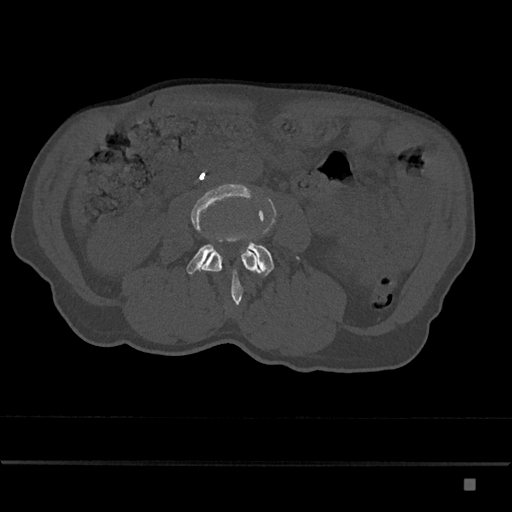
CT including the spine, one axial slice. Slice 374 of 797 in the series (ordered by position). Reconstruction kernel Br40s/3. 120 kVp. Bone window (W 1800 / L 400 HU). 0.5 mm slice thickness. 512 × 512 image matrix, field of view 390 × 390 mm. Male patient, age 72 years. From the clinical record (not read from this slice): primary cancer: prostate.
Structures marked on this image (semi-automatically segmented with operator editing):
- L3 vertebra: bounding box (x1, y1, x2, y2) in pixels: (191, 184, 261, 305)
- L4 vertebra: (186, 241, 299, 277)